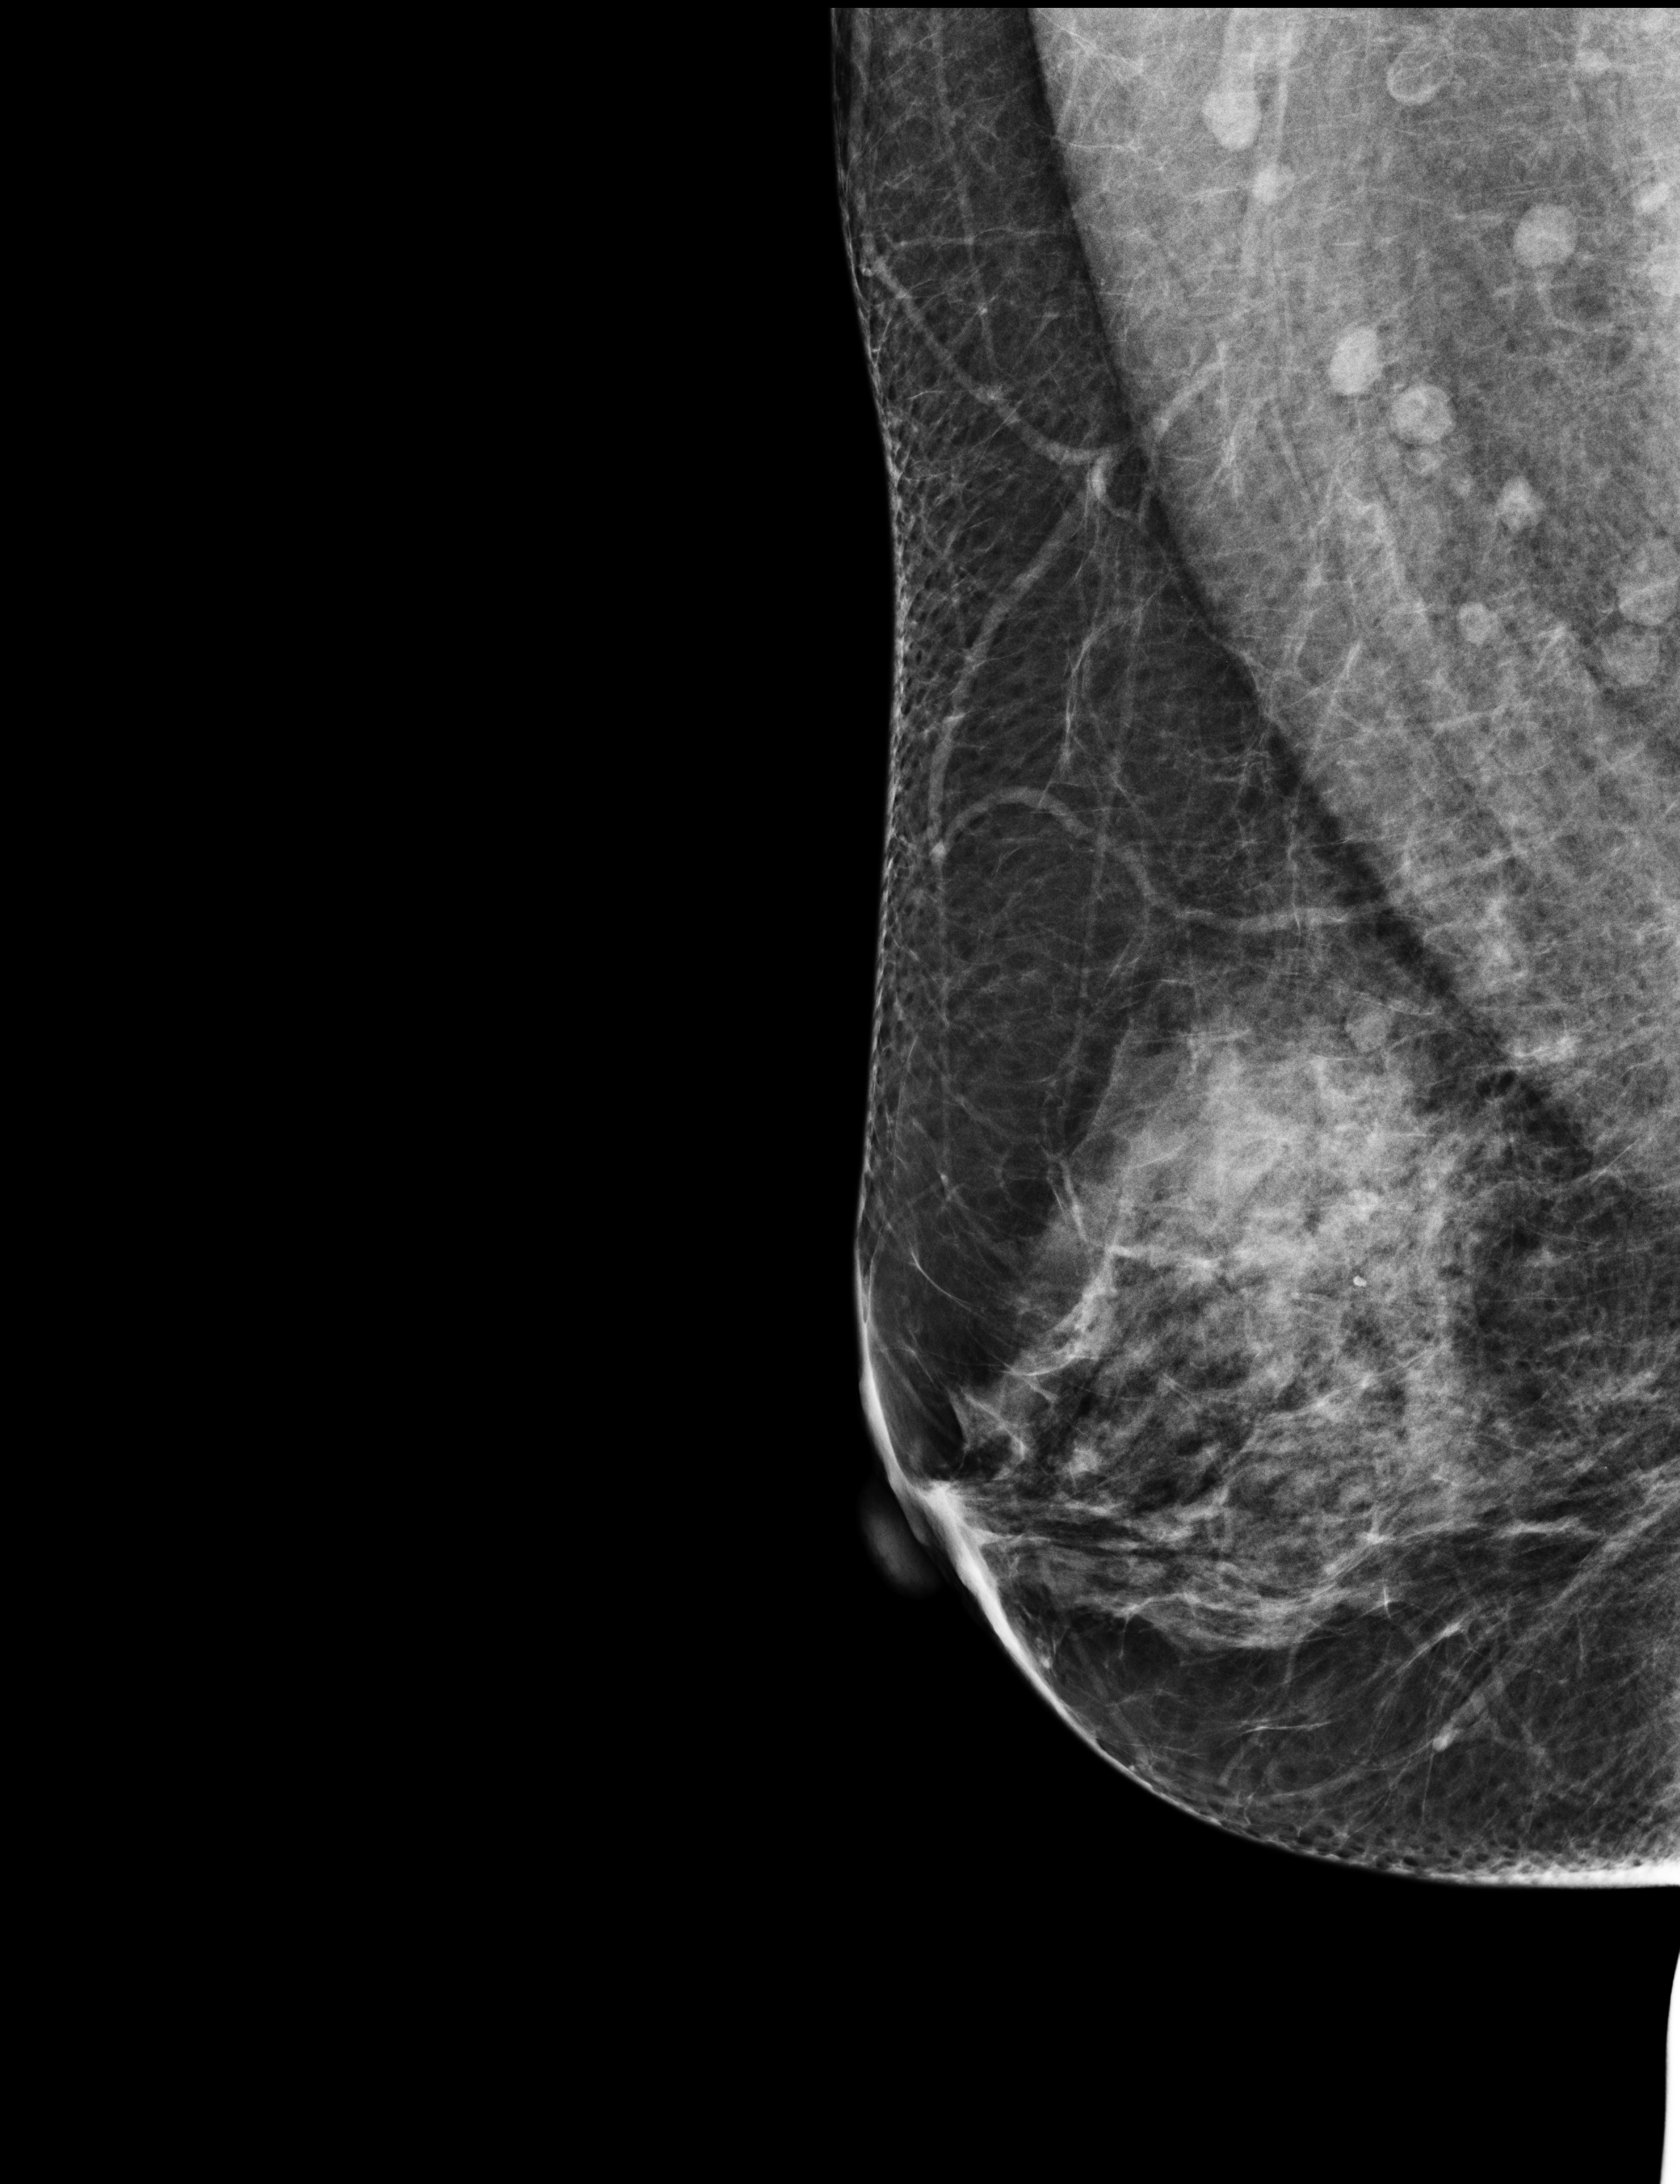
Screening examination; system: Selenia Dimensions. Female patient, age 58 years.
Image type: full-field digital mammogram. Breast: right. Projection: MLO view.